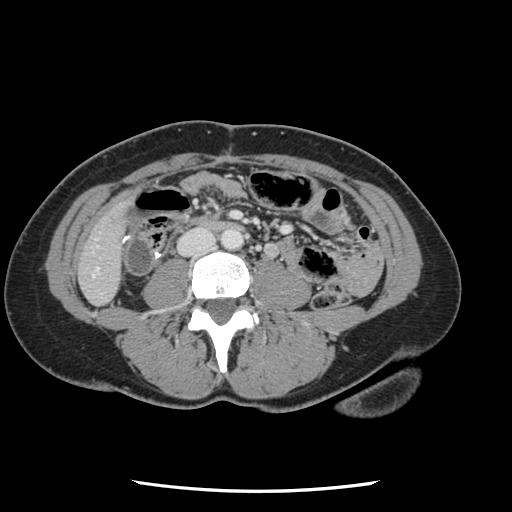
Contrast-enhanced abdominal CT, one axial slice. 120 kVp. Intravenous contrast given. Soft-tissue window (W 400 / L 40 HU). 2.5 mm slice thickness. 512 × 512 image matrix, field of view 330 × 330 mm. Female patient, age 43 years. From the clinical record (not read from this slice): diagnosis: colorectal cancer liver metastases, imaged before liver resection; multiple liver metastases: yes; largest metastasis: 3.4 cm; disease in both lobes: yes.
Structures marked on this image (outlined manually by an expert reader):
- liver: bounding box <80,206,125,305> (left, top, right, bottom; pixels)
- planned liver remnant (the part of the liver to remain after resection): <80,207,125,305>